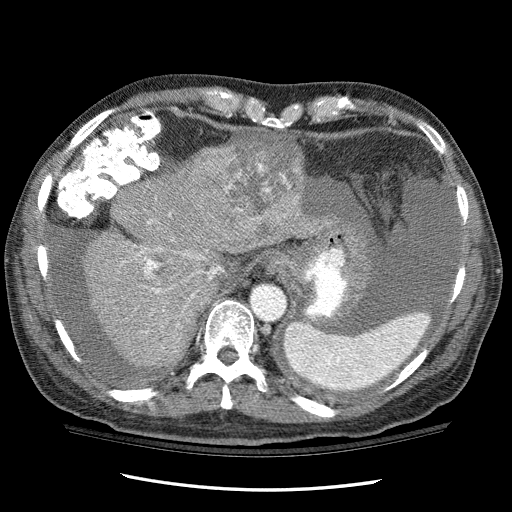
Contrast-enhanced abdominal CT (liver protocol), one axial slice. Reconstruction kernel STANDARD. One of 3 acquisitions stored at this slice position. Soft-tissue window (W 400 / L 40 HU). 2.5 mm slice thickness. 512 × 512 image matrix, field of view 360 × 360 mm. Case-level facts recorded for this patient, not image findings: diagnosis: hepatocellular carcinoma (patient treated with transarterial chemoembolisation; whether this scan precedes or follows treatment is not stated here); TNM stage (as recorded): Stage-I; Child-Pugh class: C; tumour differentiation: well differentiated; tumour nodularity: uninodular.
Structures marked on this image (semi-automatically segmented with operator editing):
- liver parenchyma outside the tumour (the mass and vessels are separate outlines, so this box may not span the whole liver): bounding box [x1, y1, x2, y2] px = [82, 146, 345, 368]
- mass: [188, 130, 305, 245]
- liver vessels: [141, 214, 199, 332]